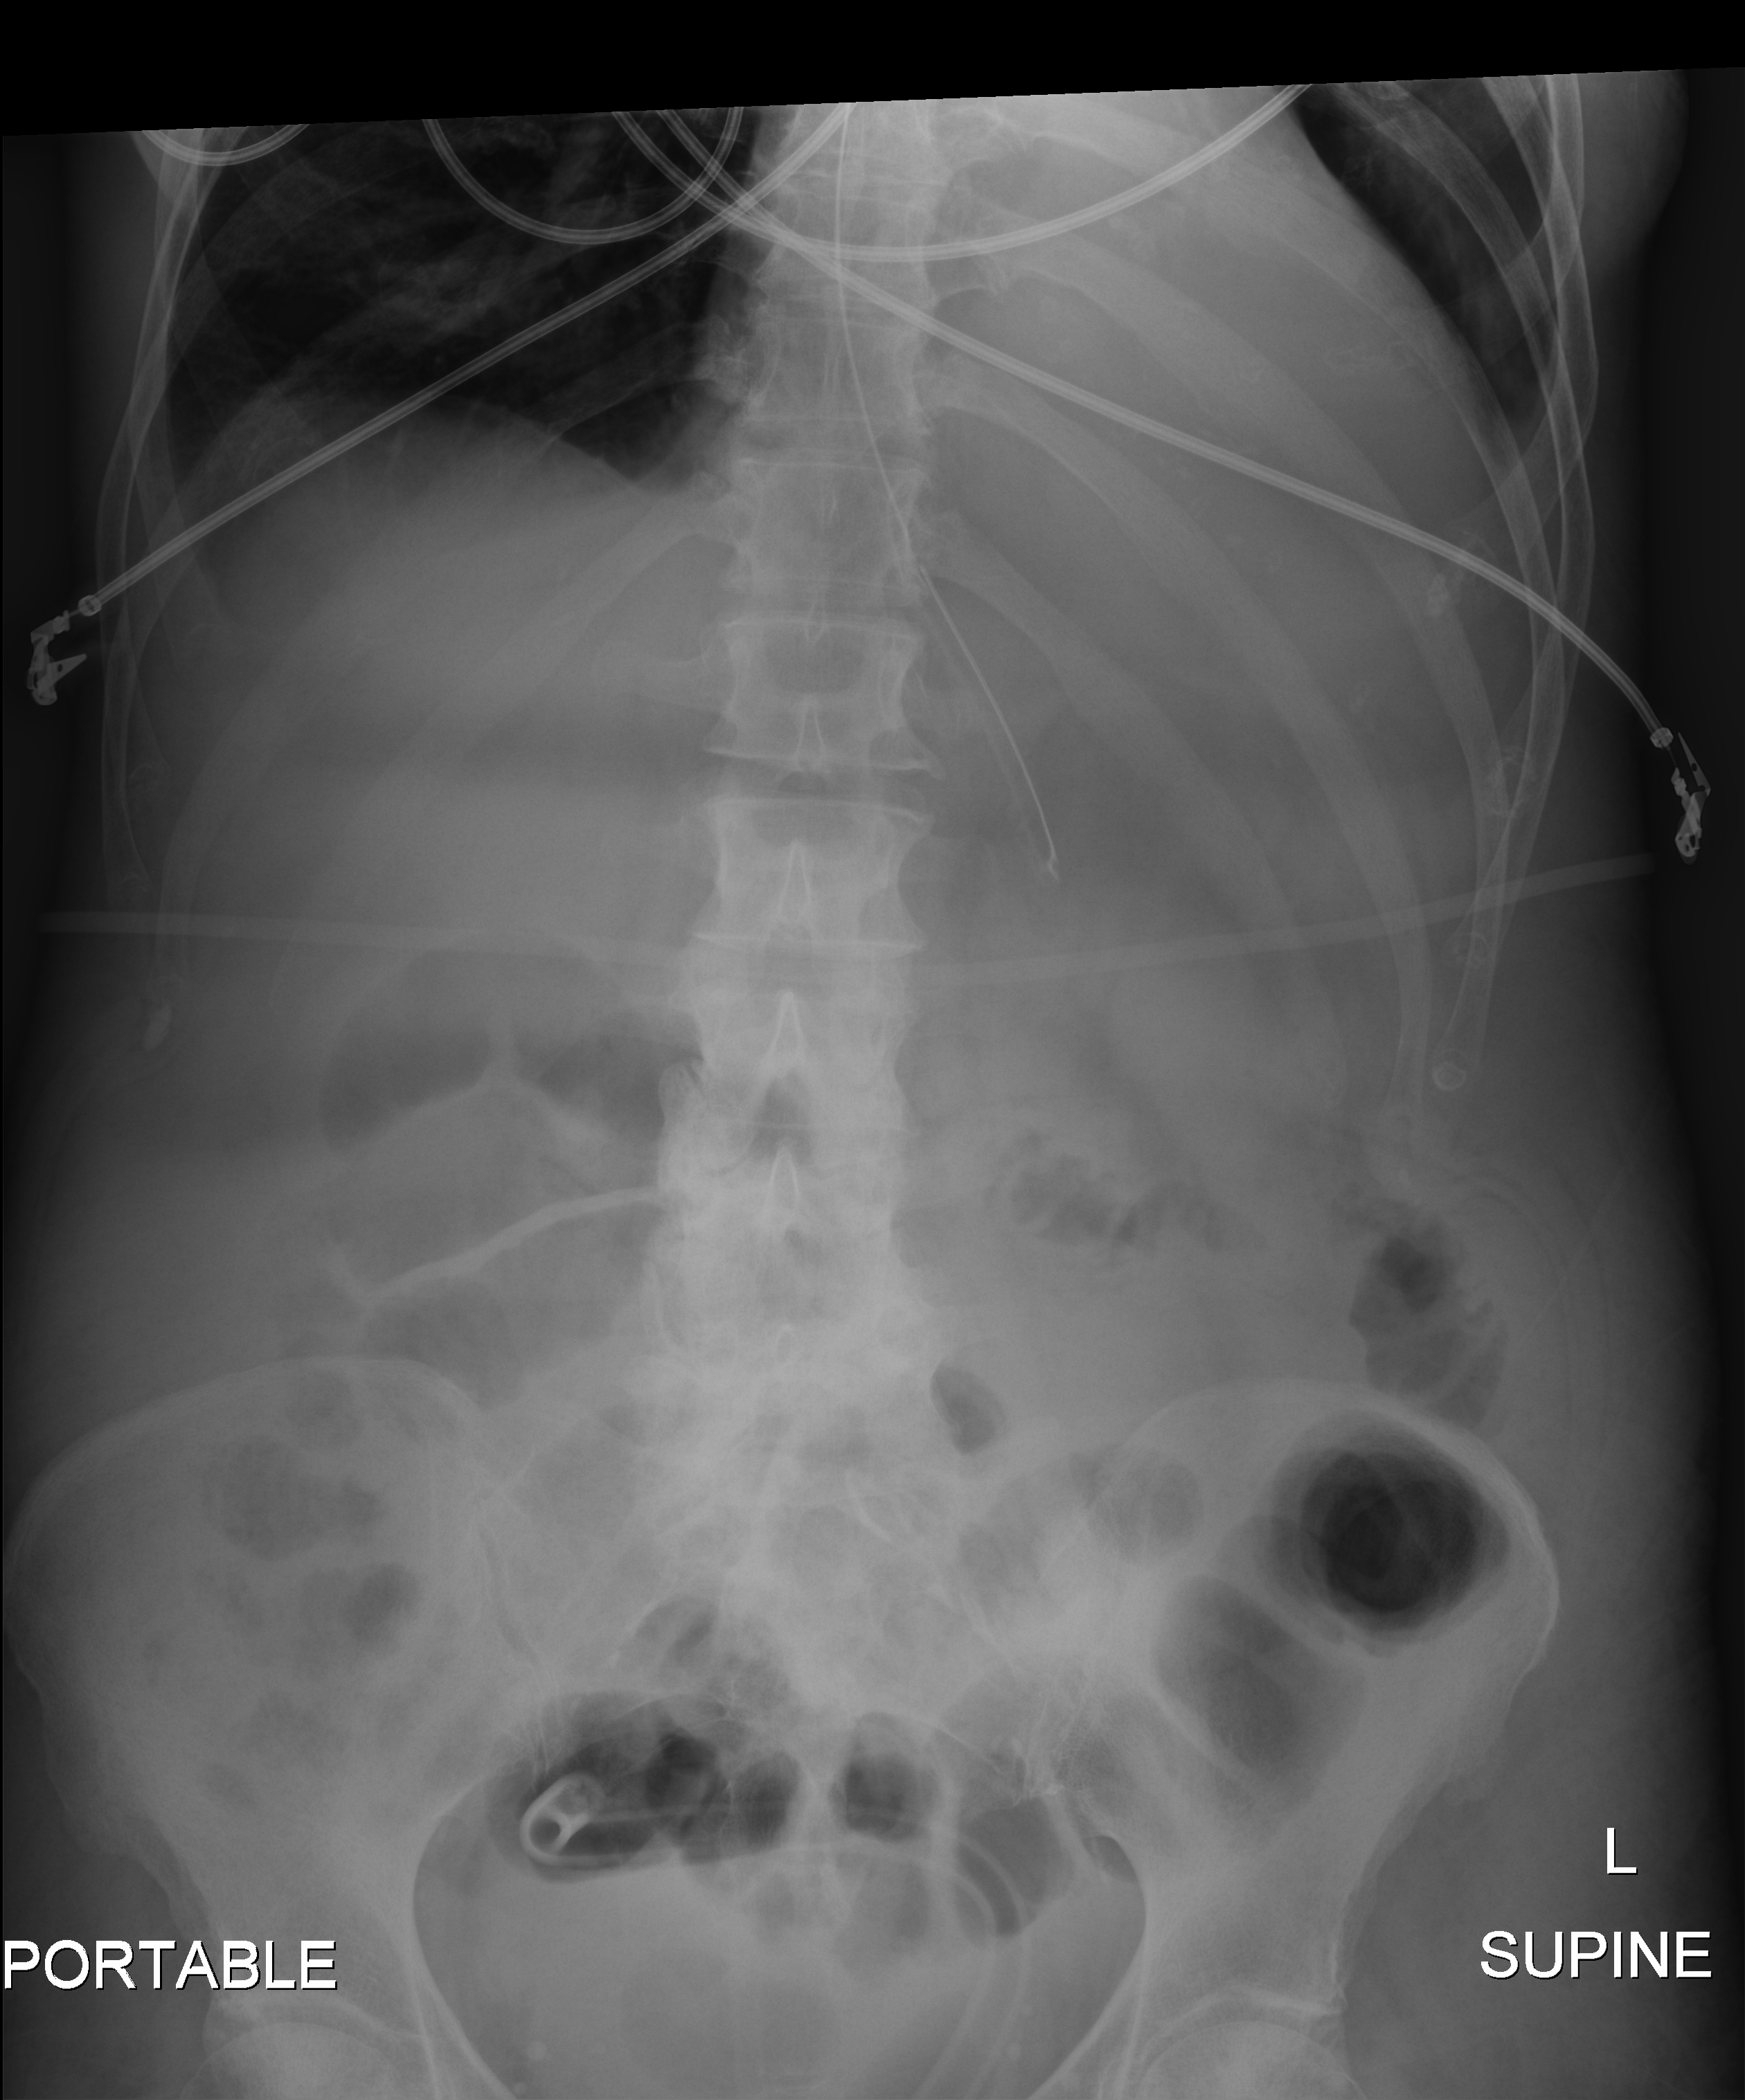
Abdomen X-ray (portable). Female patient hospitalised with COVID-19, age 60–74 years.
Hospital-stay facts (about this admission, not read from this image; timing relative to this image not recorded): admitted to intensive care during this hospital stay: yes; mechanically ventilated during this hospital stay: yes.